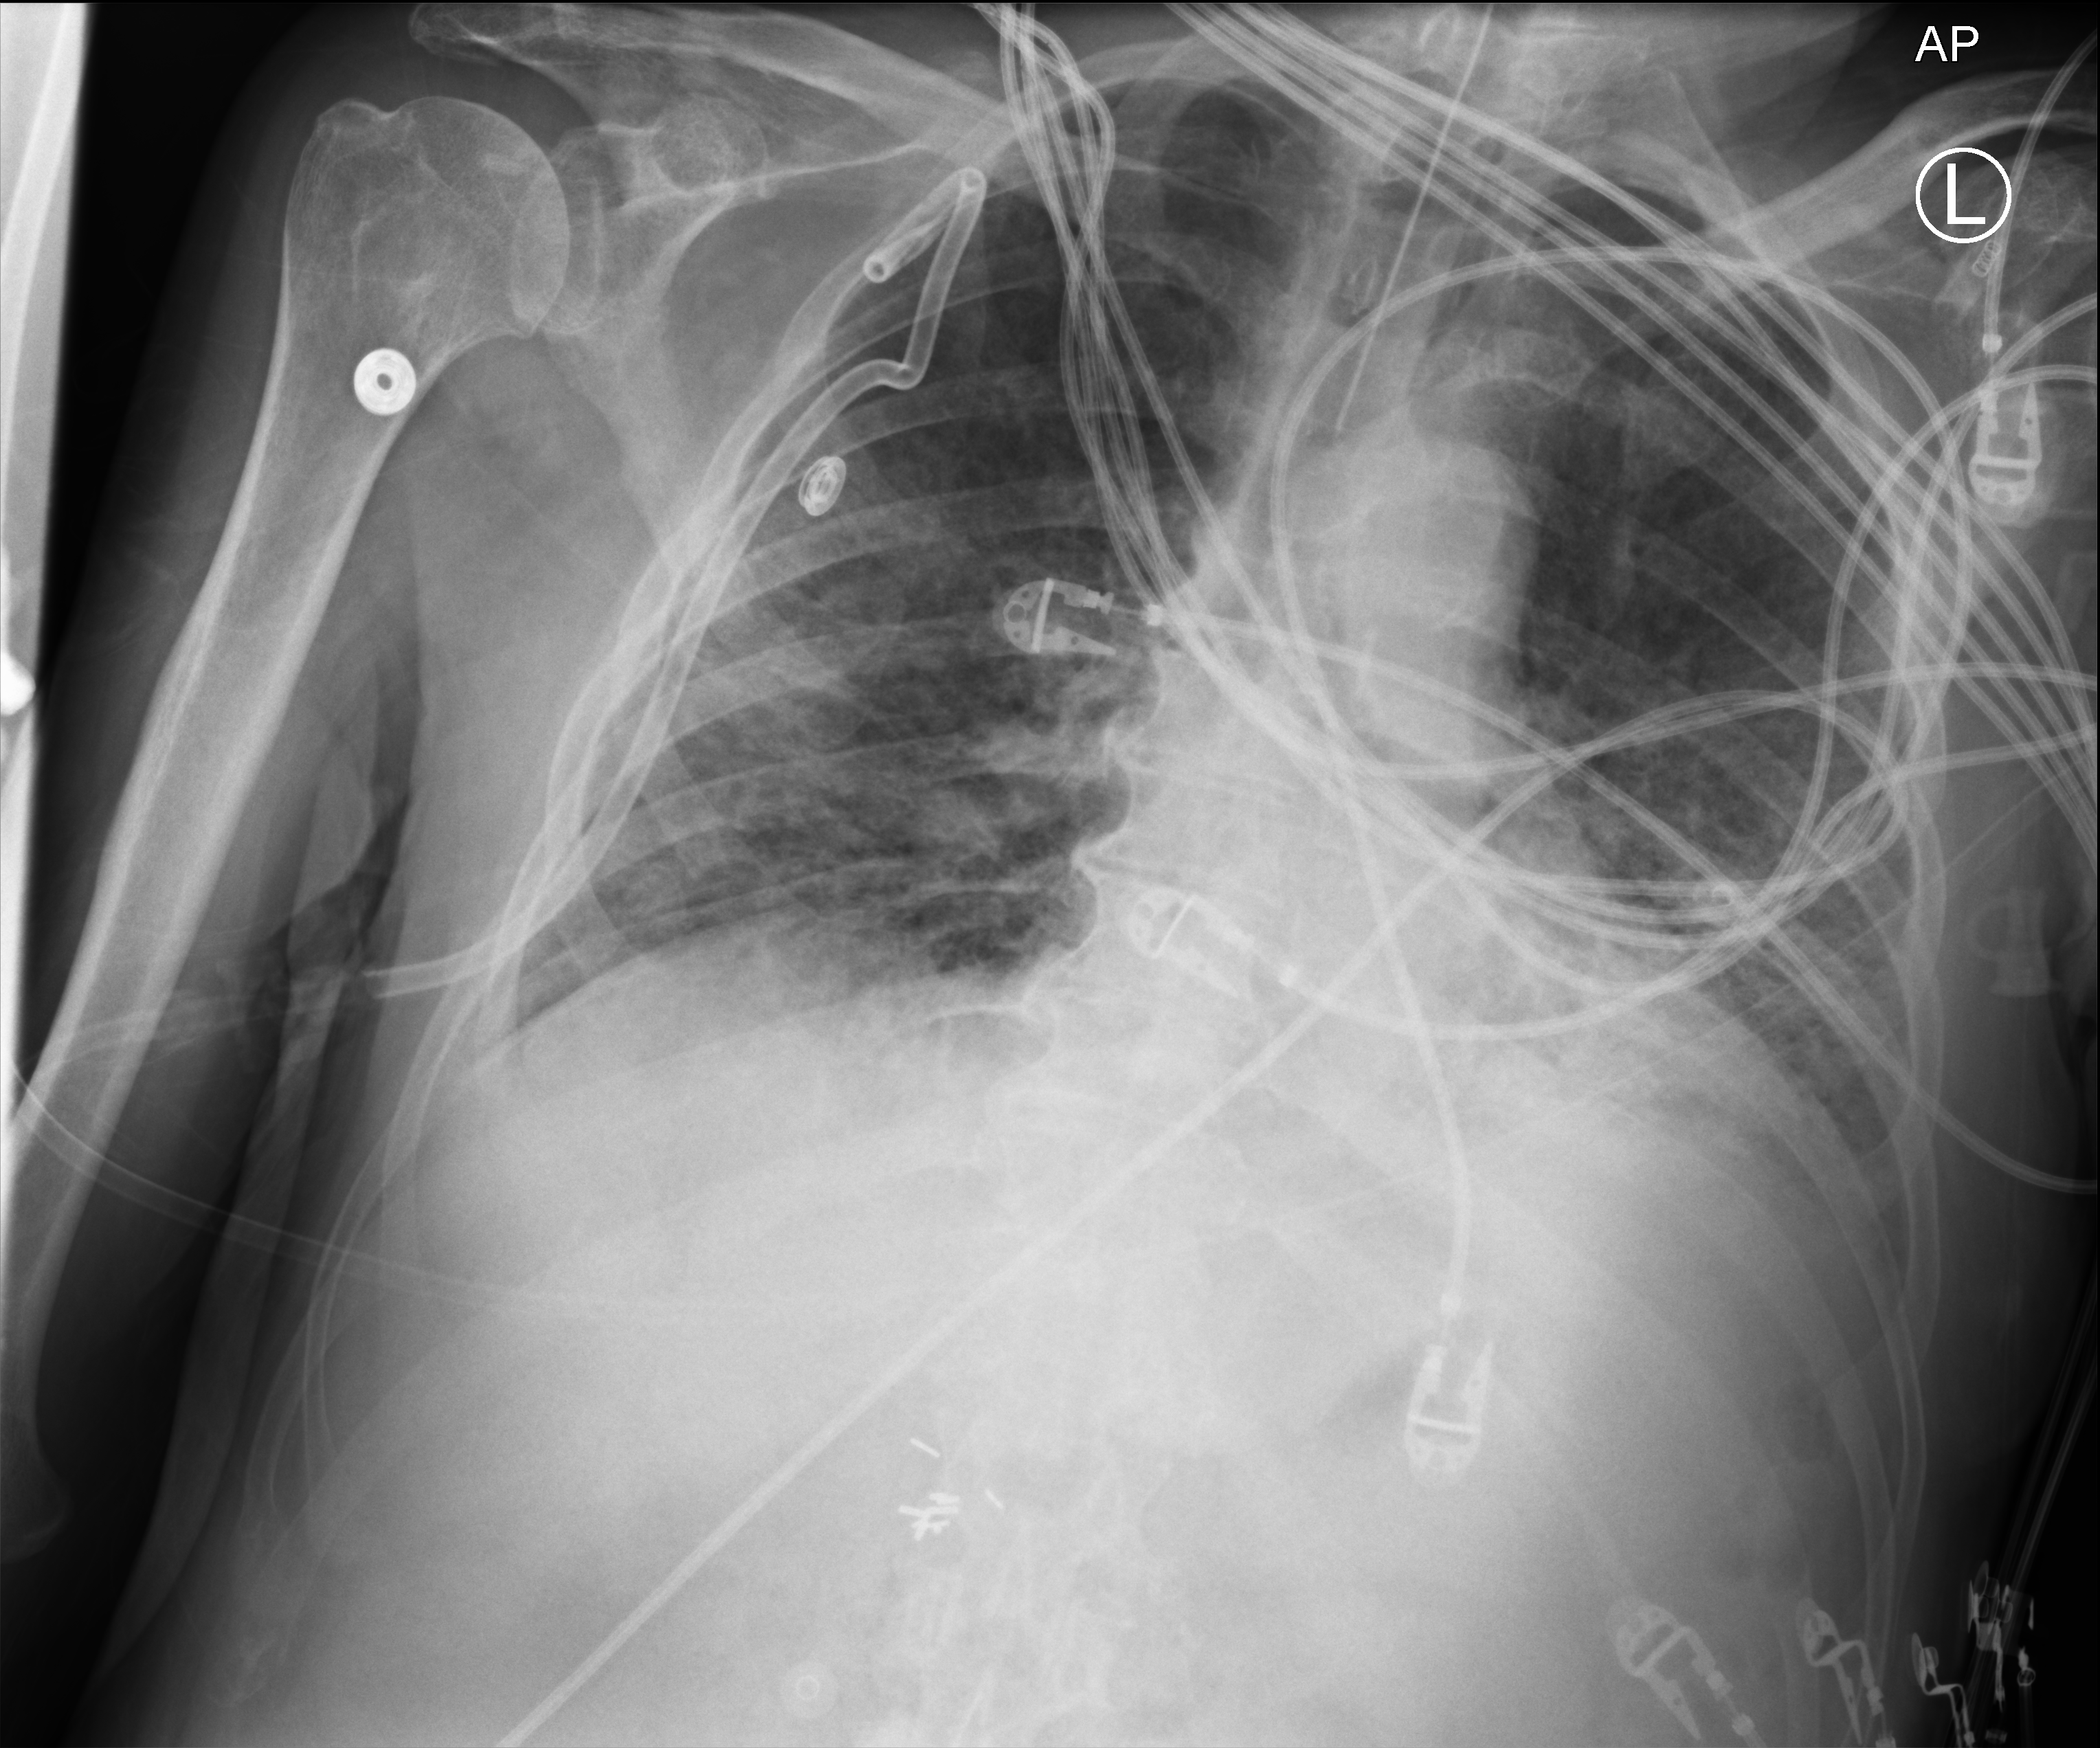
Chest X-ray (portable). Patient hospitalised with COVID-19; male, aged 75–90 years.
Admission-level facts for this patient (not findings on this image; timing relative to this image not recorded): mechanically ventilated during this hospital stay: yes.